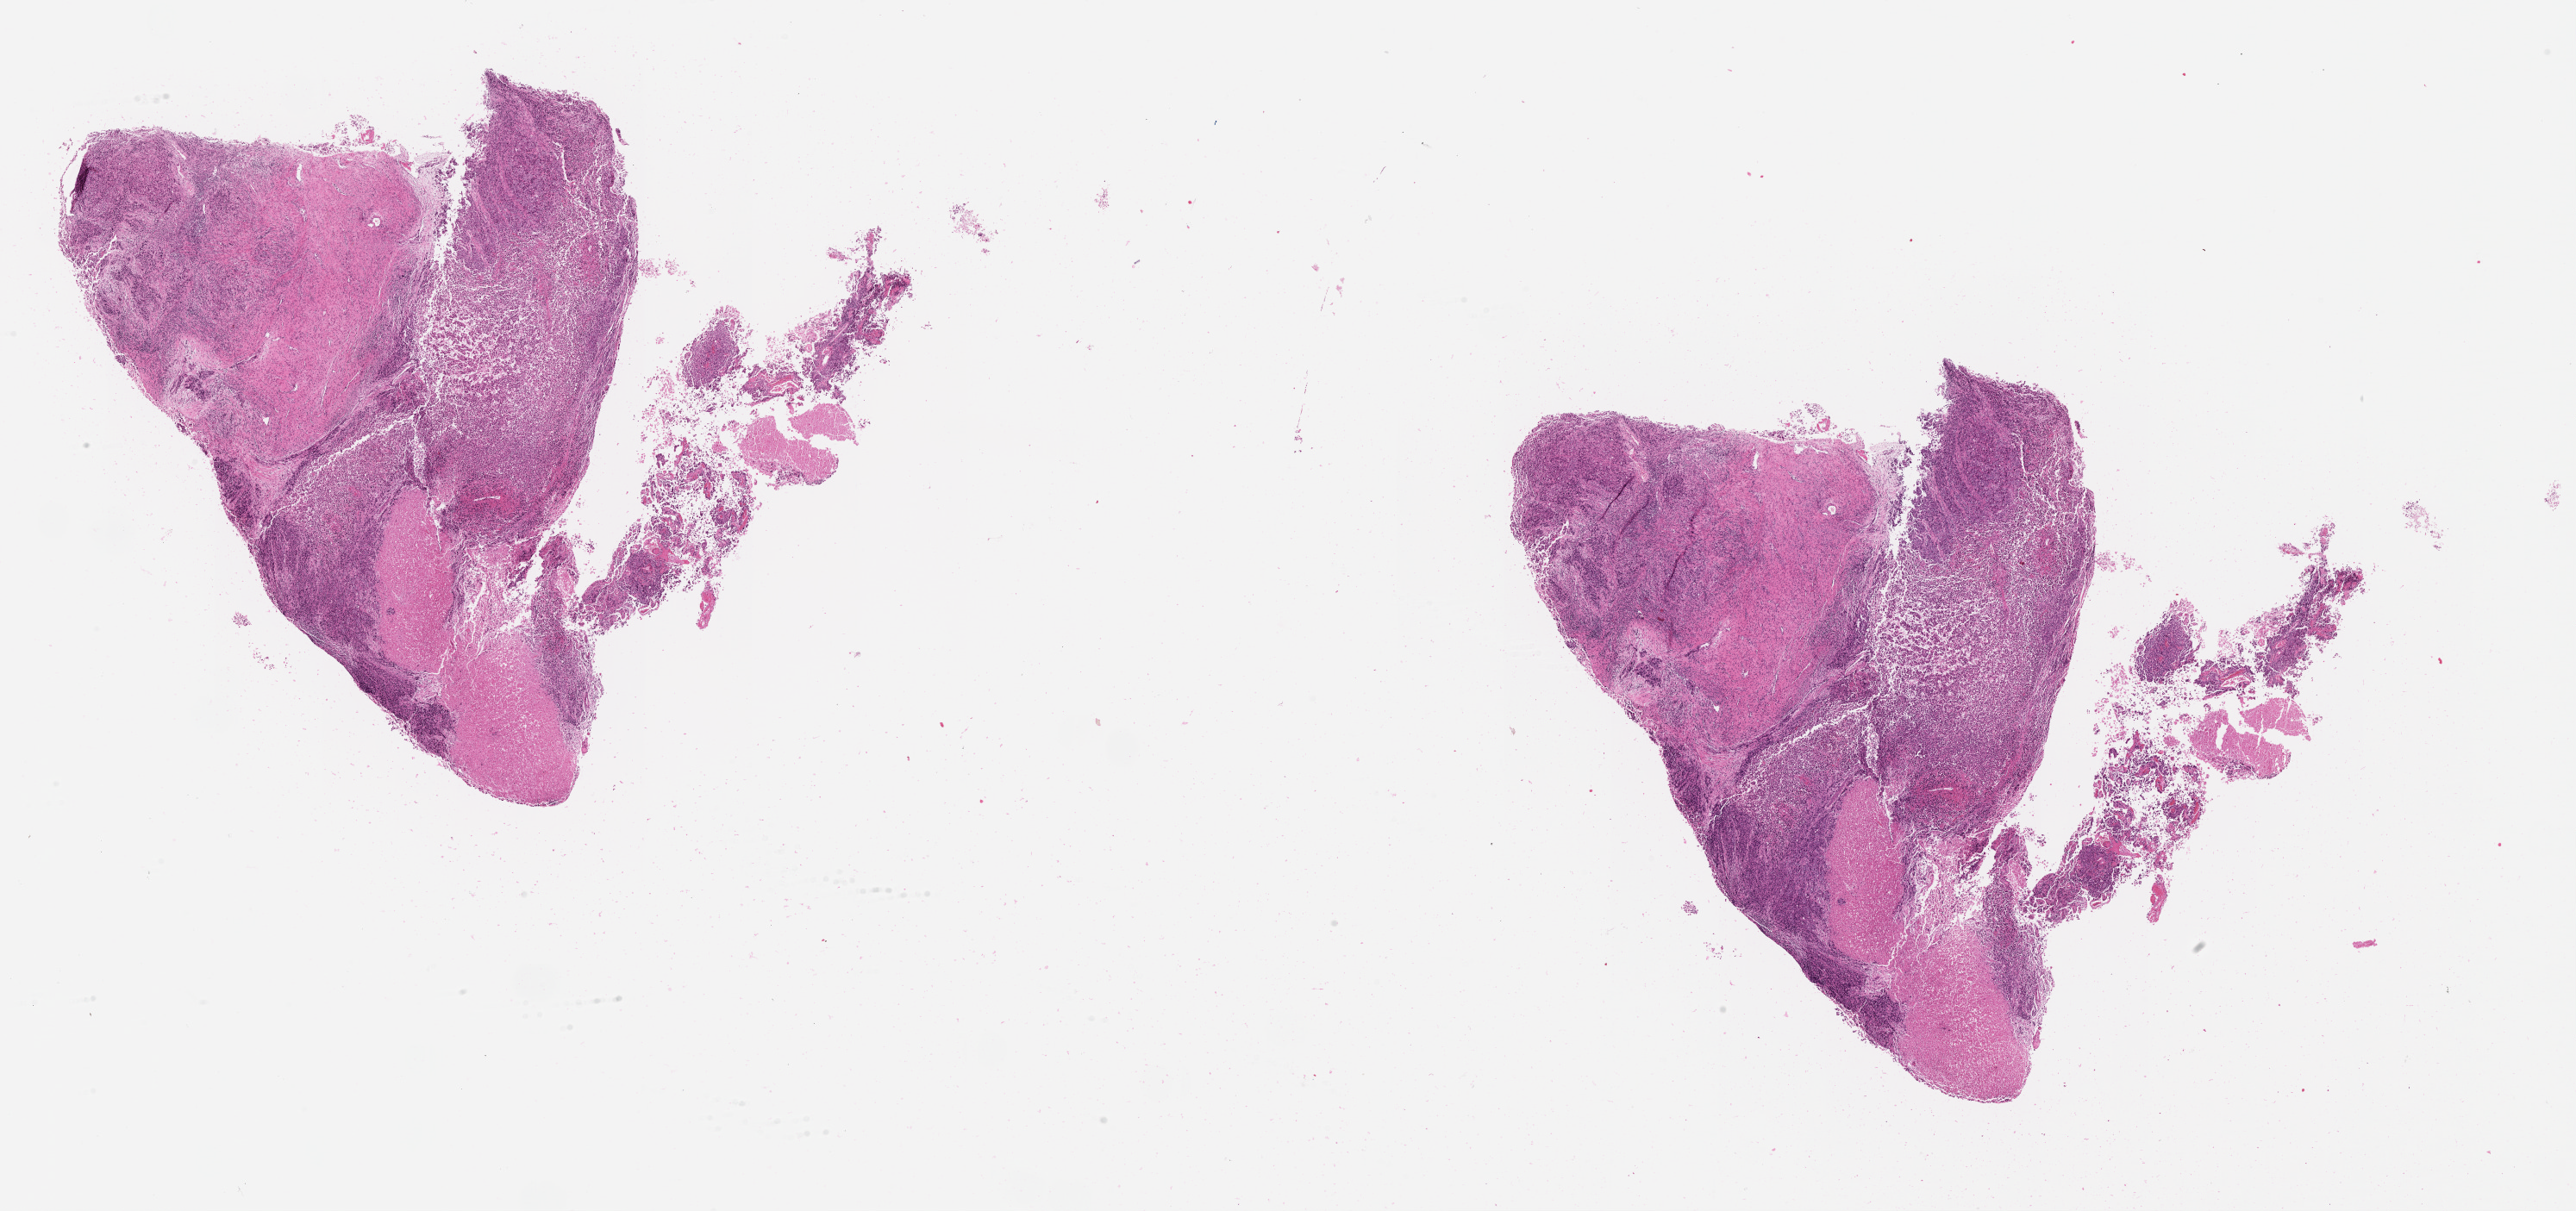
H&E whole-slide image, a low-resolution overview of the entire scanned area, about 24.1 x 11.3 mm (from a 20x scan); uterus, tumour tissue. Female, 64 y/o. Histologic grade: G3 (poorly differentiated).
* AJCC pathologic stage: IIIC2
* histologic diagnosis: Endometrioid adenocarcinoma, NOS